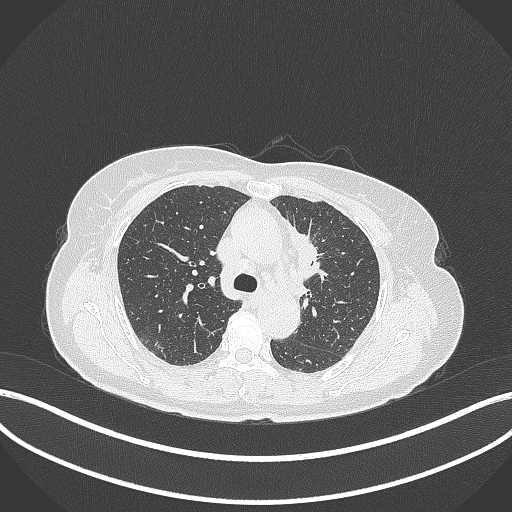
Chest CT, one axial slice. Reconstruction kernel B70f. Lung window (W 1500 / L -600 HU). 1 mm slice thickness. 512 × 512 image matrix, field of view 400 × 400 mm. Patient: female, 65 years. From the clinical record (not read from this slice): clinical TNM (as recorded): T2a N0 M0; histopathological grade: G2-3.
Outlined on this slice (bounding box drawn by a radiologist):
- lung tumour (recorded histology: adenocarcinoma): box from (x=283, y=217) to (x=326, y=280) px